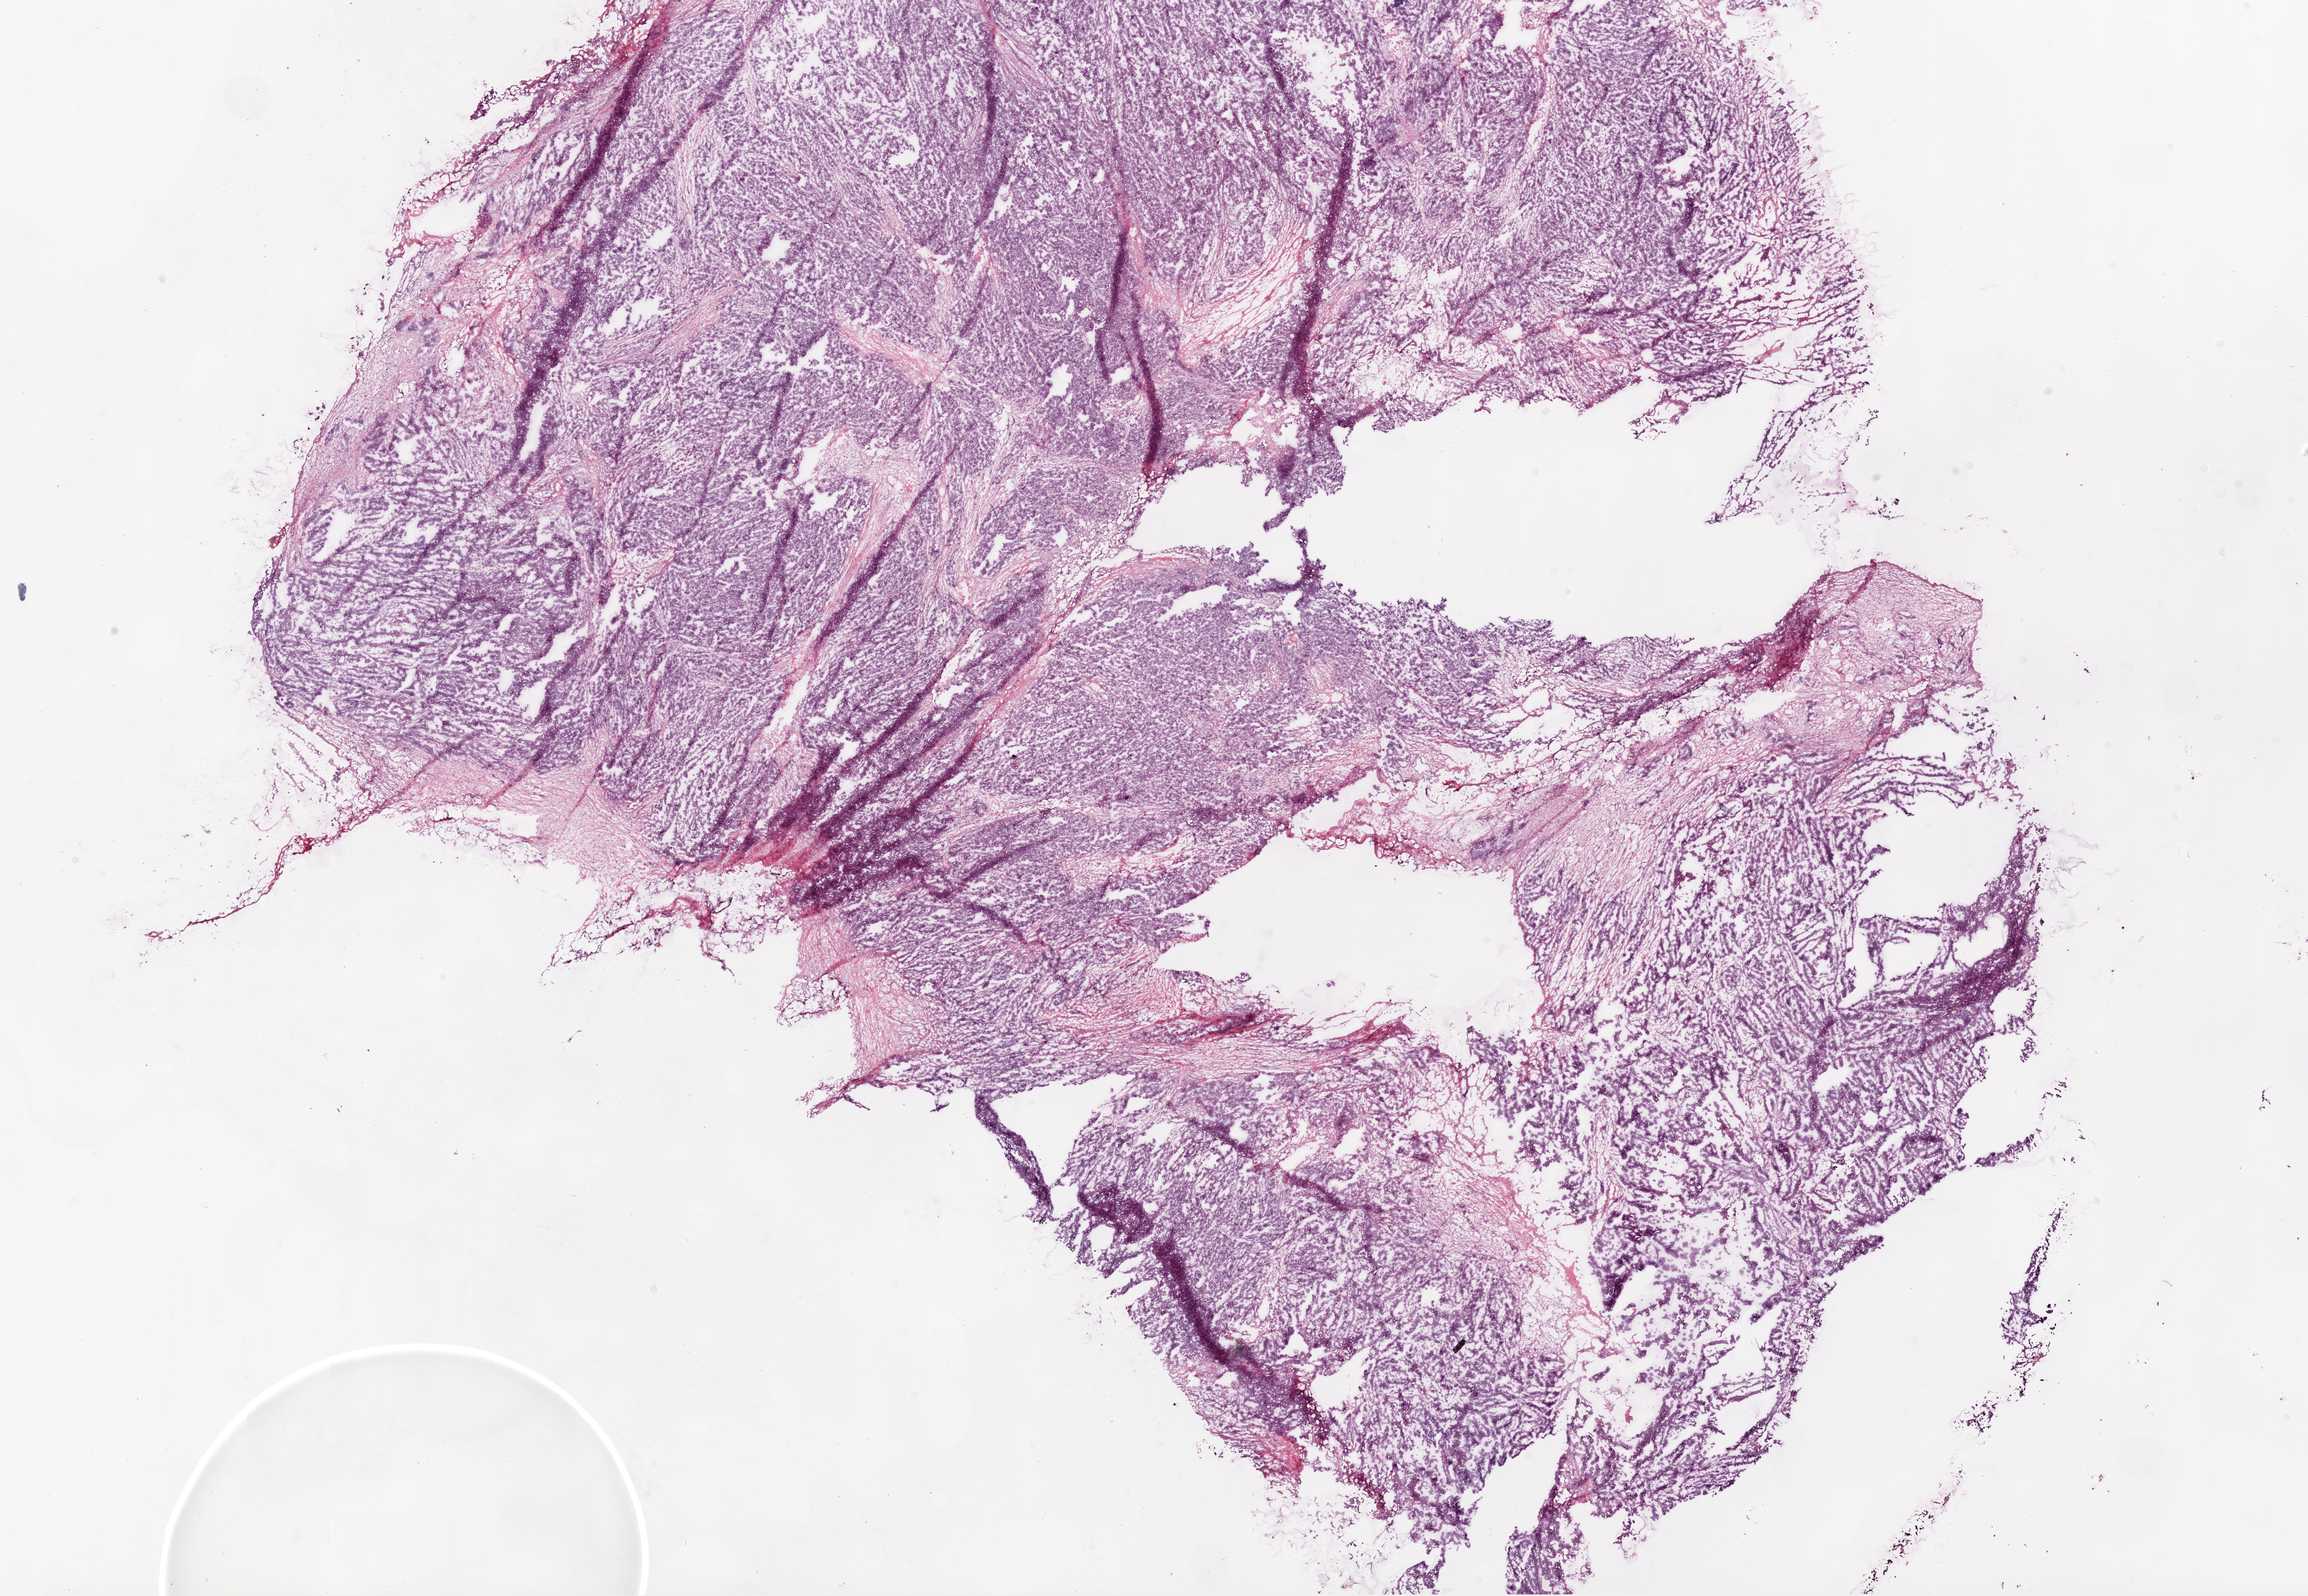
Whole-slide histology image, H&E-stained — whole scanned area (about 28.1 x 19.4 mm) shown as a low-resolution overview, frozen section from the bottom of the tissue portion, primary tumour sample from the ovary. Patient: female, age at initial diagnosis 63 years. Histologic grade: G3 (poorly differentiated). Composition of this section per pathologist review: tumour cells 85%, tumour nuclei 85%, normal cells 0%, stromal cells 15%, necrosis 0%. Infiltration values recorded for this section: lymphocyte infiltration 5%, monocyte infiltration 0%, neutrophil infiltration 0%.
FIGO stage: IV. Laterality: bilateral. Diagnosis: Serous cystadenocarcinoma, NOS.